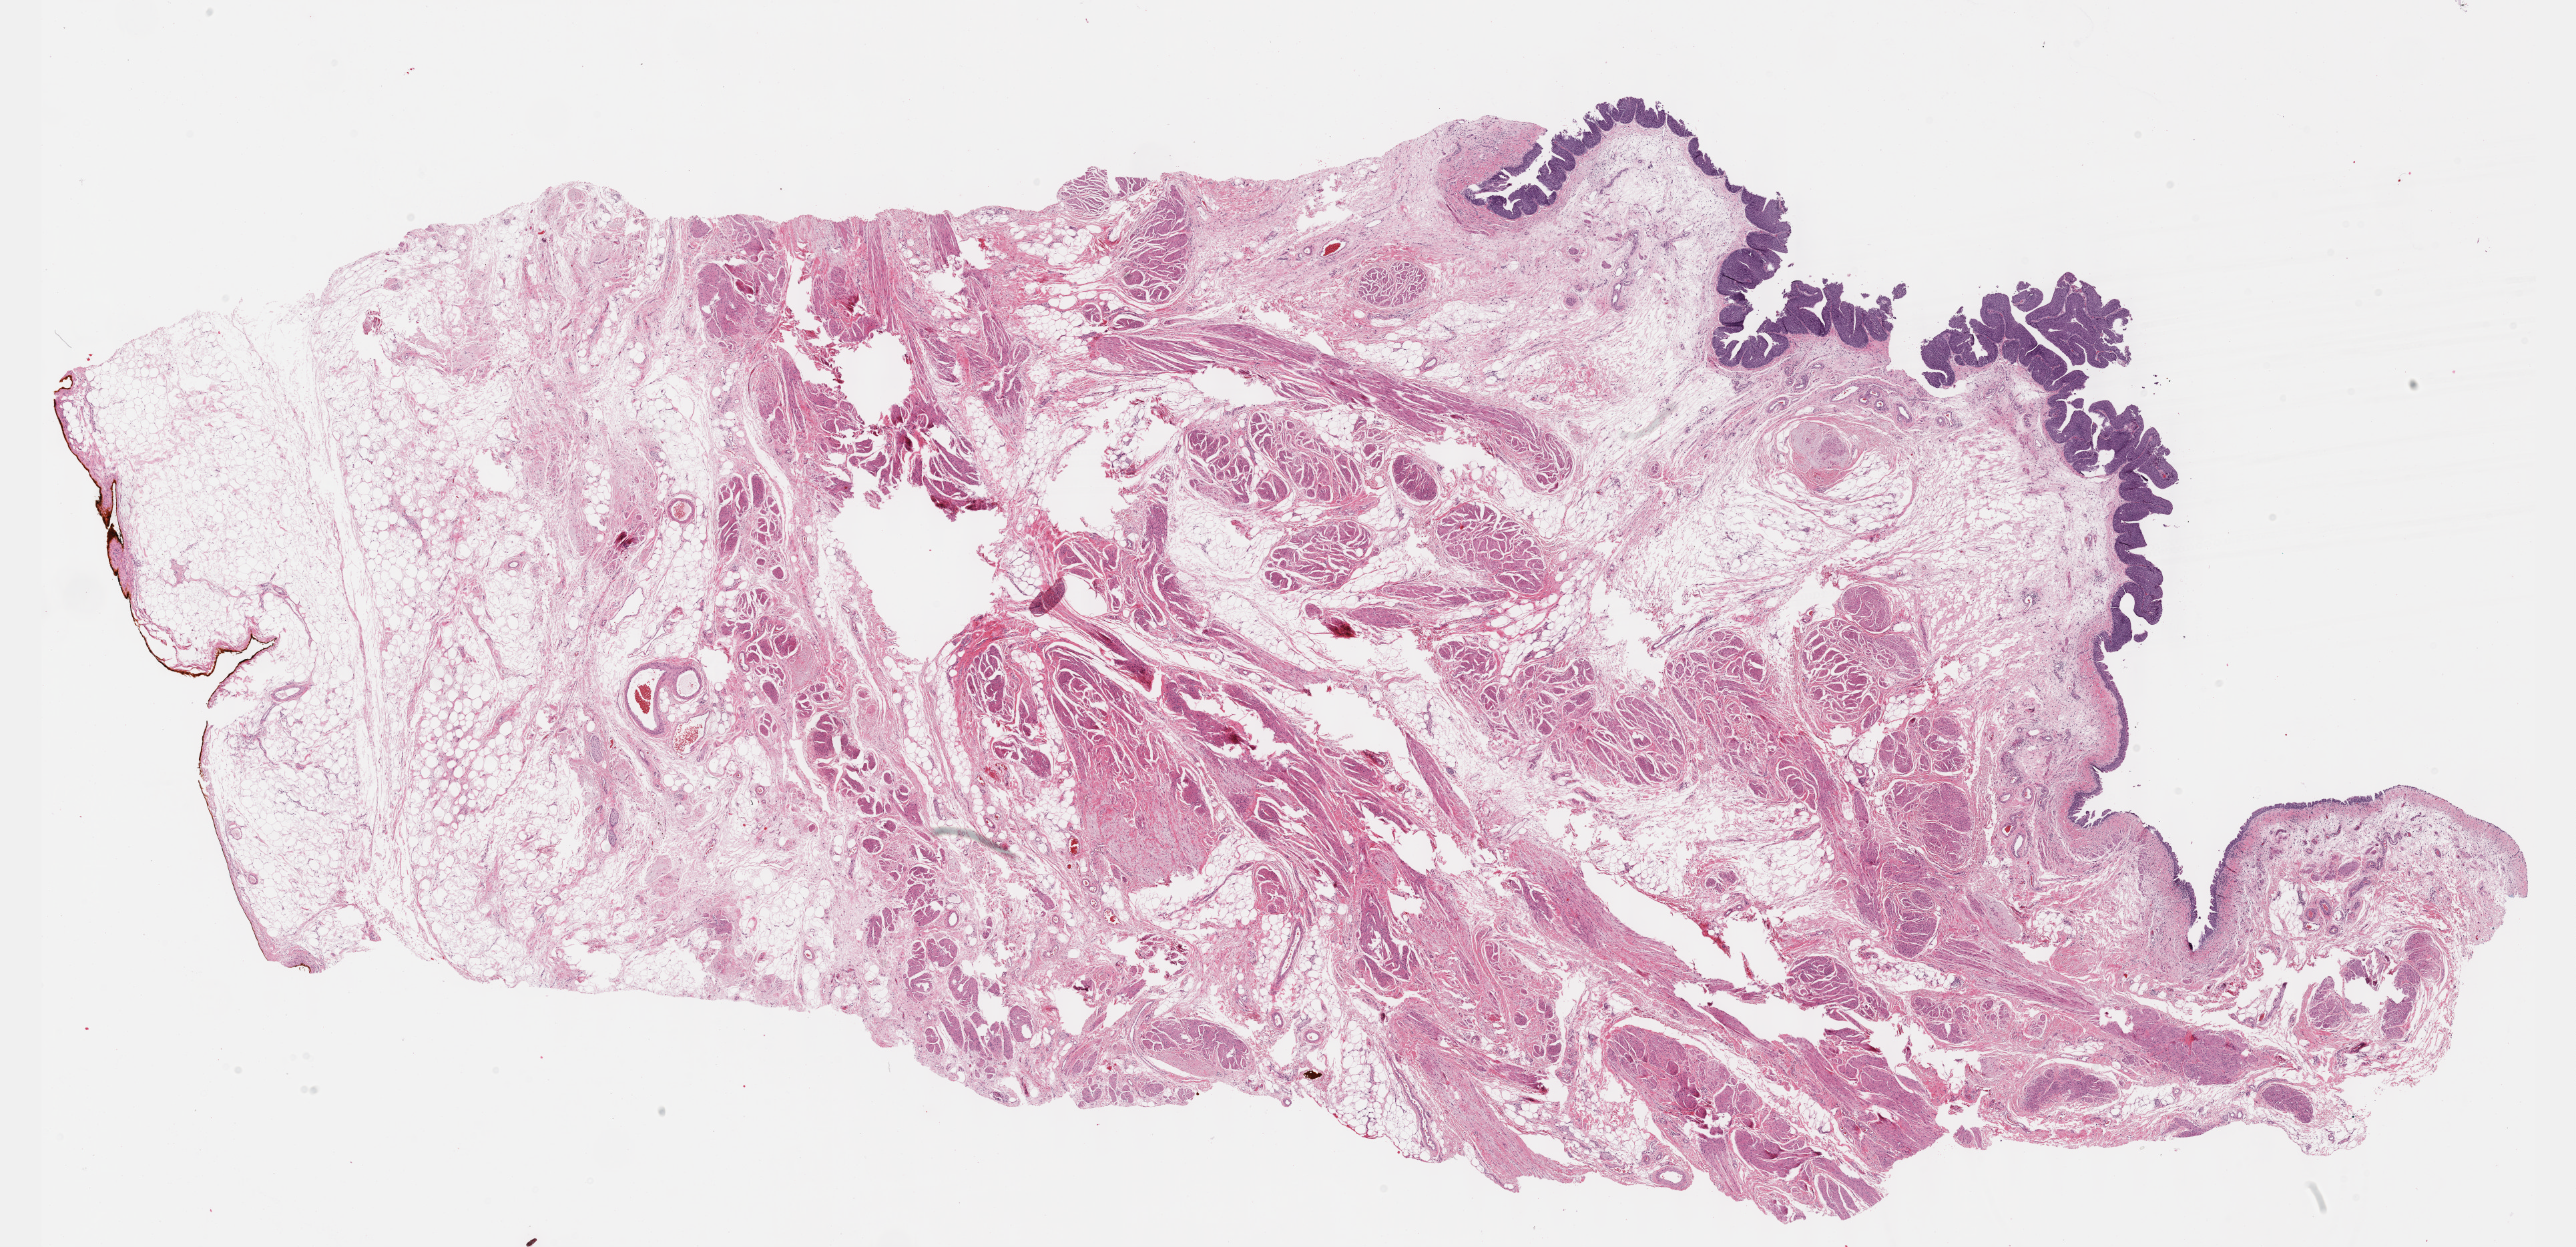
Whole-slide histology image, H&E — a low-resolution overview of the entire scanned area, about 31.2 x 15.1 mm (acquisition: 40x scan), formalin-fixed paraffin-embedded (FFPE) diagnostic section, sample: primary tumour, bladder. Patient: male, age at initial diagnosis 72 years.
Diagnosis: Transitional cell carcinoma (lateral wall of bladder).